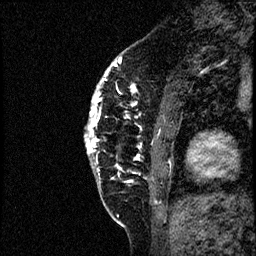
Breast MRI (dynamic contrast-enhanced), one sagittal slice; slice 14 of 60 in the series (ordered by position); dynamic contrast-enhanced study with each time point stored as its own series, time point 2 of 4 at this slice position (early post-contrast, ordered by acquisition time); 1.5 T; TE 4.2 ms, TR 17.6 ms; 2 mm slice thickness; 256 × 256 image matrix. Female patient, age 40 years. From the clinical record (not read from this slice): setting: breast cancer imaged before/during neoadjuvant chemotherapy; receptor status: HER2-positive.
Annotated regions visible in this slice (semi-automatically segmented with operator editing):
- analysis volume of interest (the breast-tissue region the enhancement analysis was run in; not a lesion): bounding box [x1, y1, x2, y2] px = [86, 56, 197, 205]
- tumour enhancement mask (voxels above the 100 % enhancement threshold inside the analysis volume of interest): [86, 56, 155, 202]